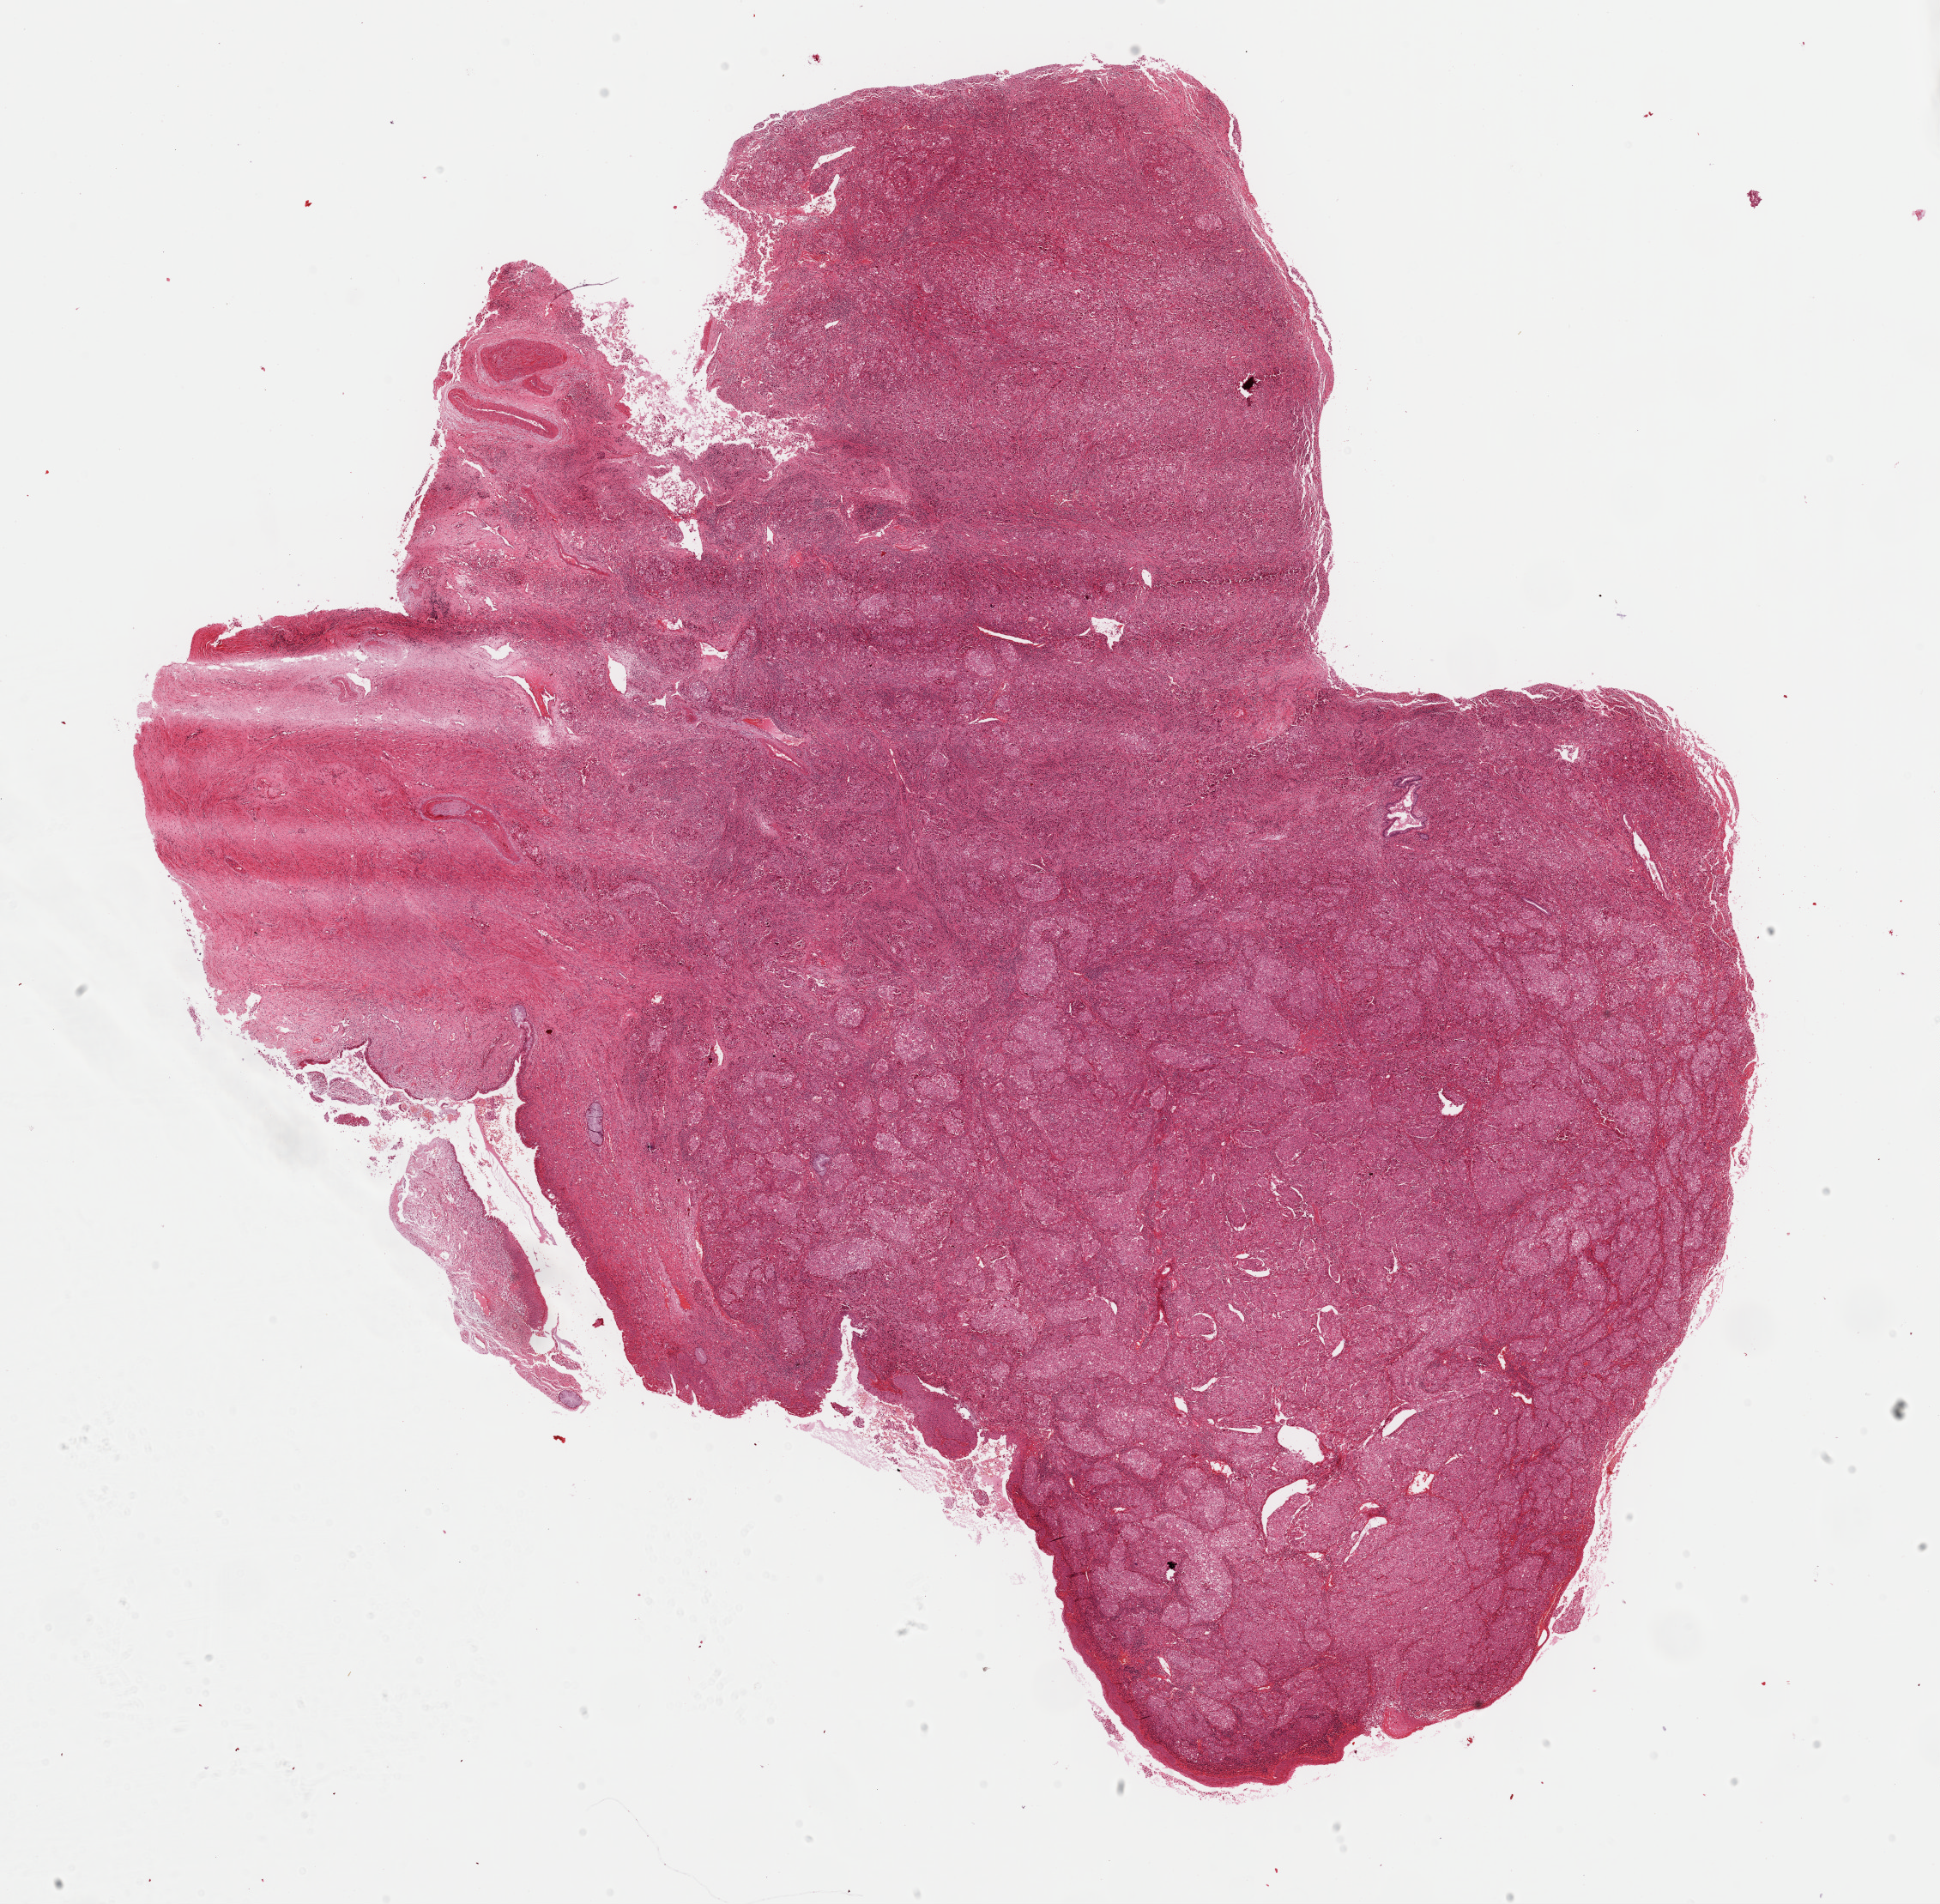
Whole-slide histology image, H&E, shown as a low-resolution overview of the whole scanned area (about 17.9 x 17.5 mm, slide scanned at 40x). FFPE section. Sample: primary tumour, cervix. Patient: female, age at initial diagnosis 35 years. Histologic grade: G3 (poorly differentiated).
FIGO stage: IIIB. Pathologic diagnosis: Squamous cell carcinoma, NOS (cervix uteri).